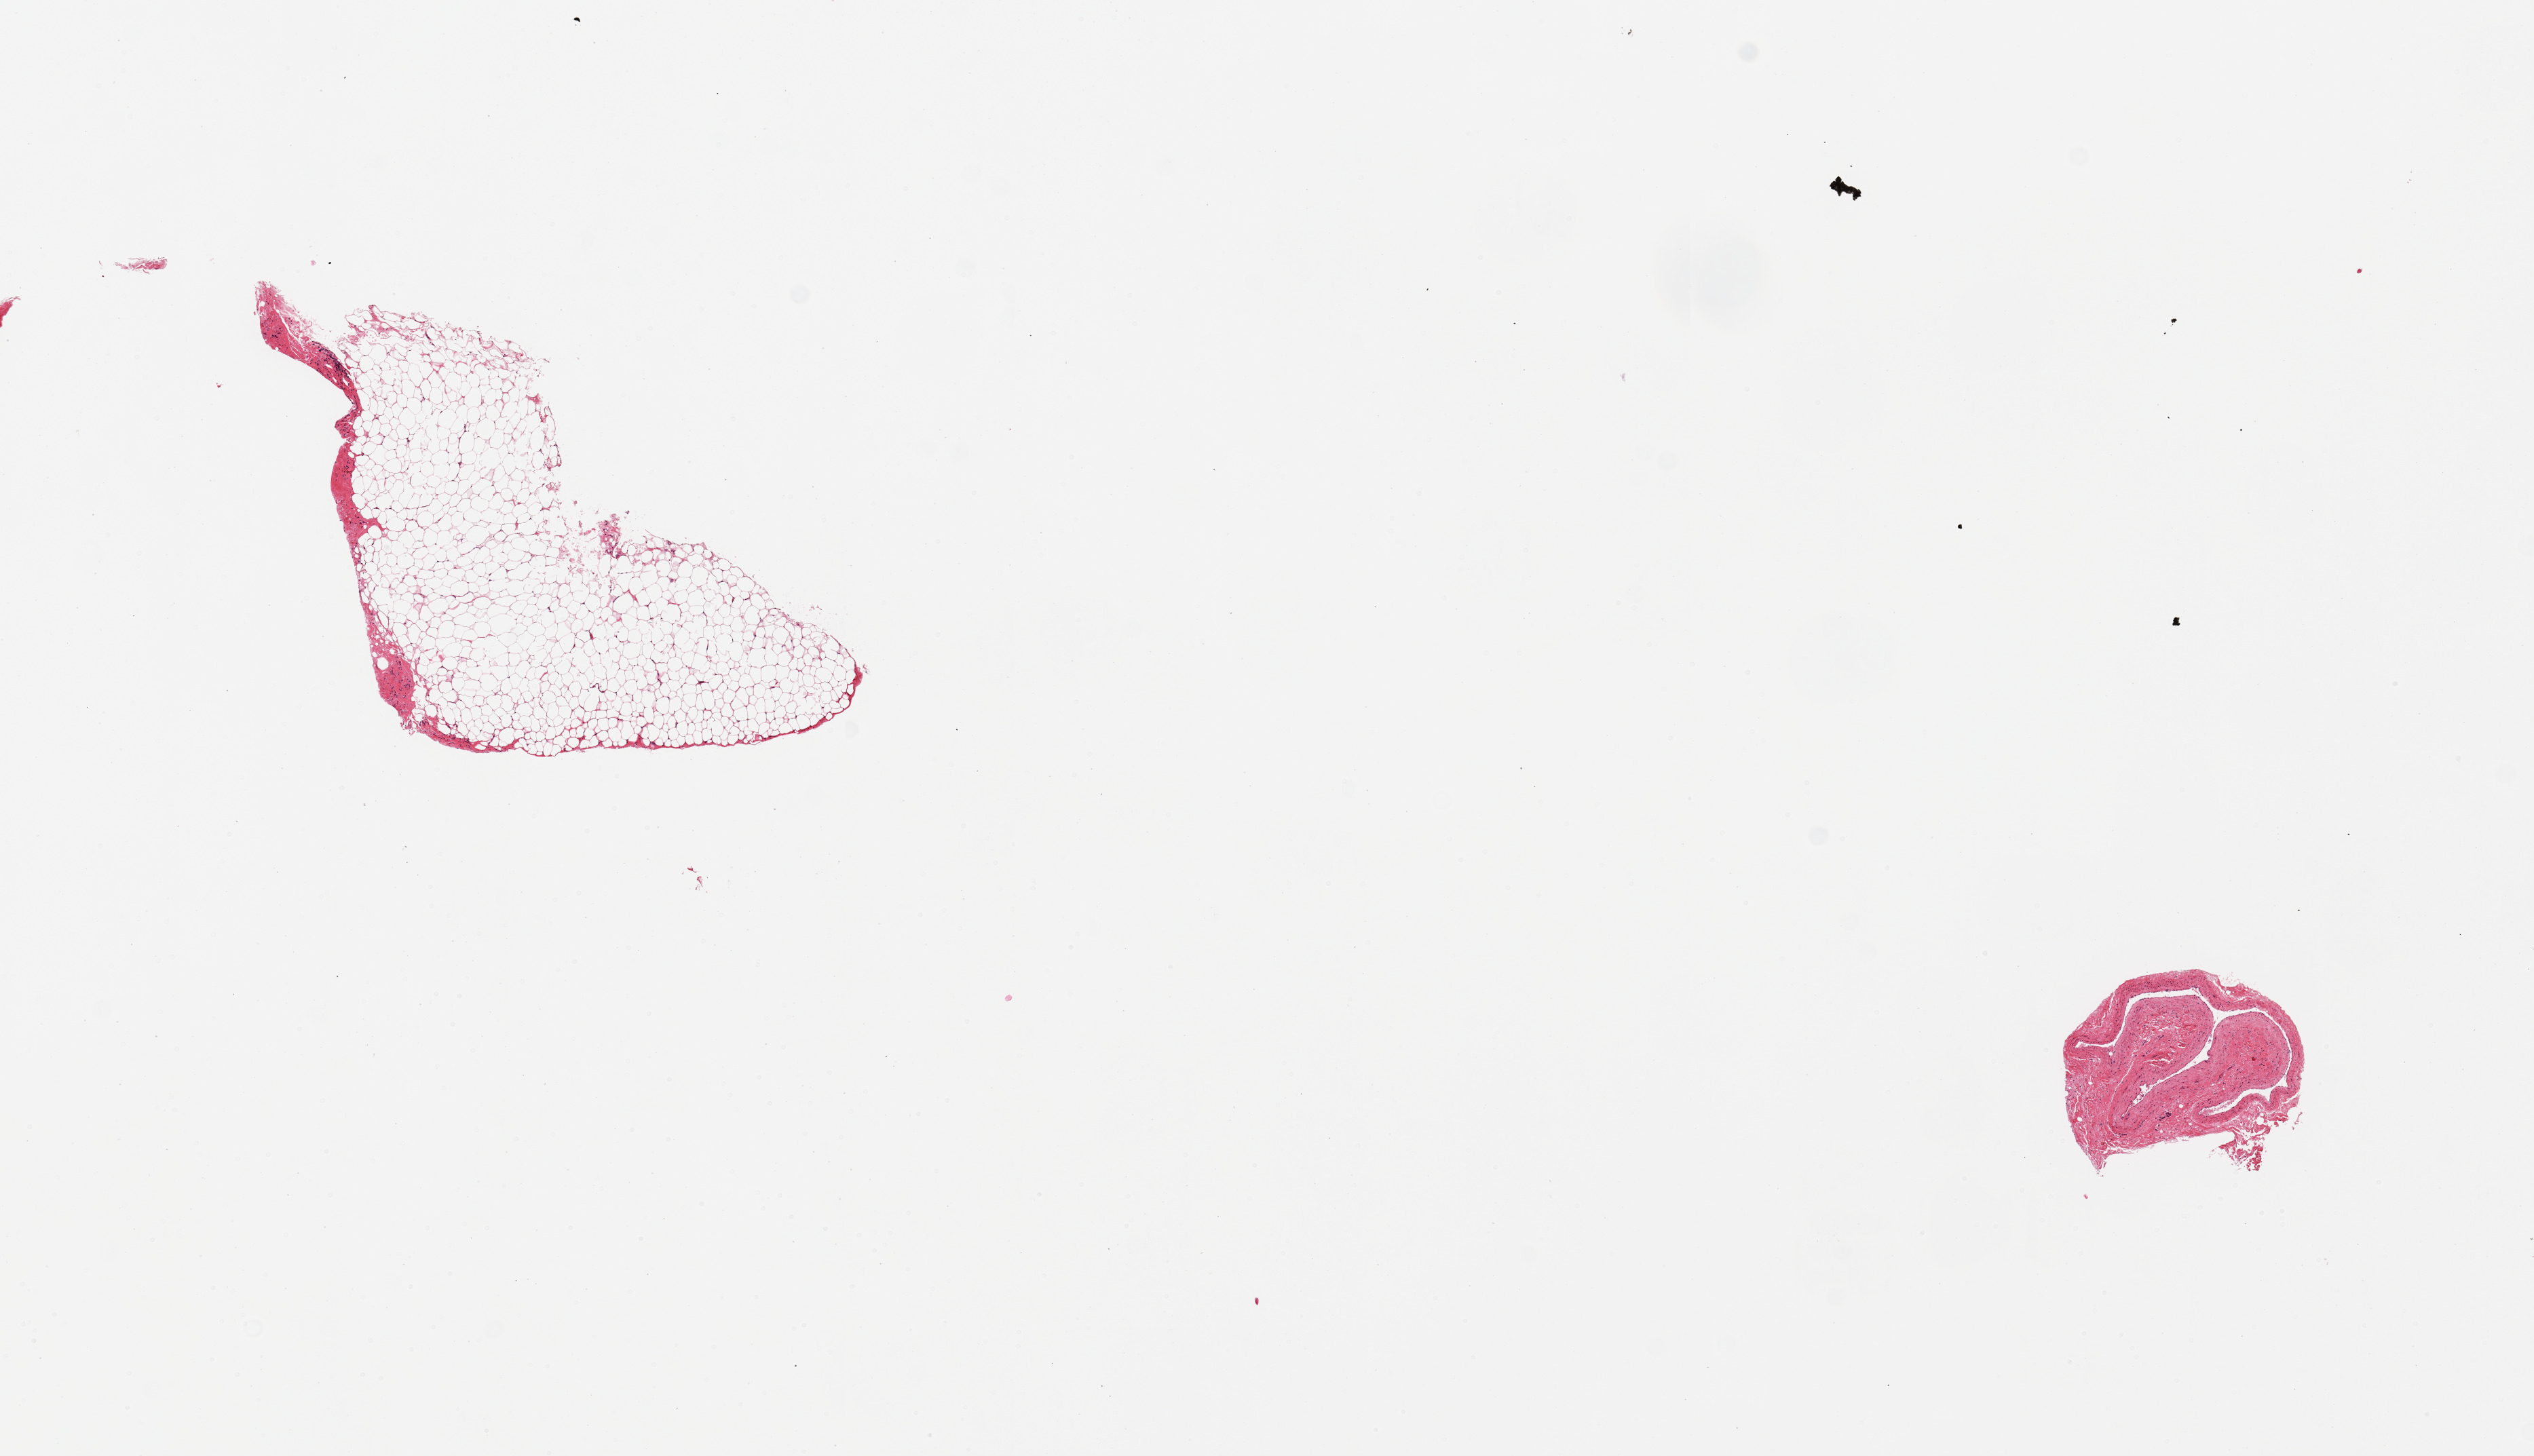
H&E whole-slide image, a low-resolution overview of the entire scanned area, about 14.8 x 8.5 mm (from a 20x scan), PAXgene-fixed paraffin-embedded (PFPE) section, sampled site (target tissue): coronary artery, donor tissue sample.
Reviewer comment on this tissue sample: 2 pieces; one is fat, second is vein.